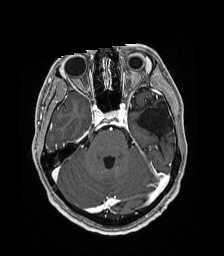
Brain MRI from a brain-tumour surgery series, one axial slice. Position 124 of 192 along the scan axis. T1-weighted post-contrast. 224 × 256 image matrix. From the clinical record (not read from this slice): histopathology: Low grade glioma; IDH mutation: no; tumour location: Left Parieto-Occipital Intraventricular.
Annotated regions visible in this slice (expert manual segmentation):
- previous resection cavity: box from (x=136, y=102) to (x=172, y=136) px